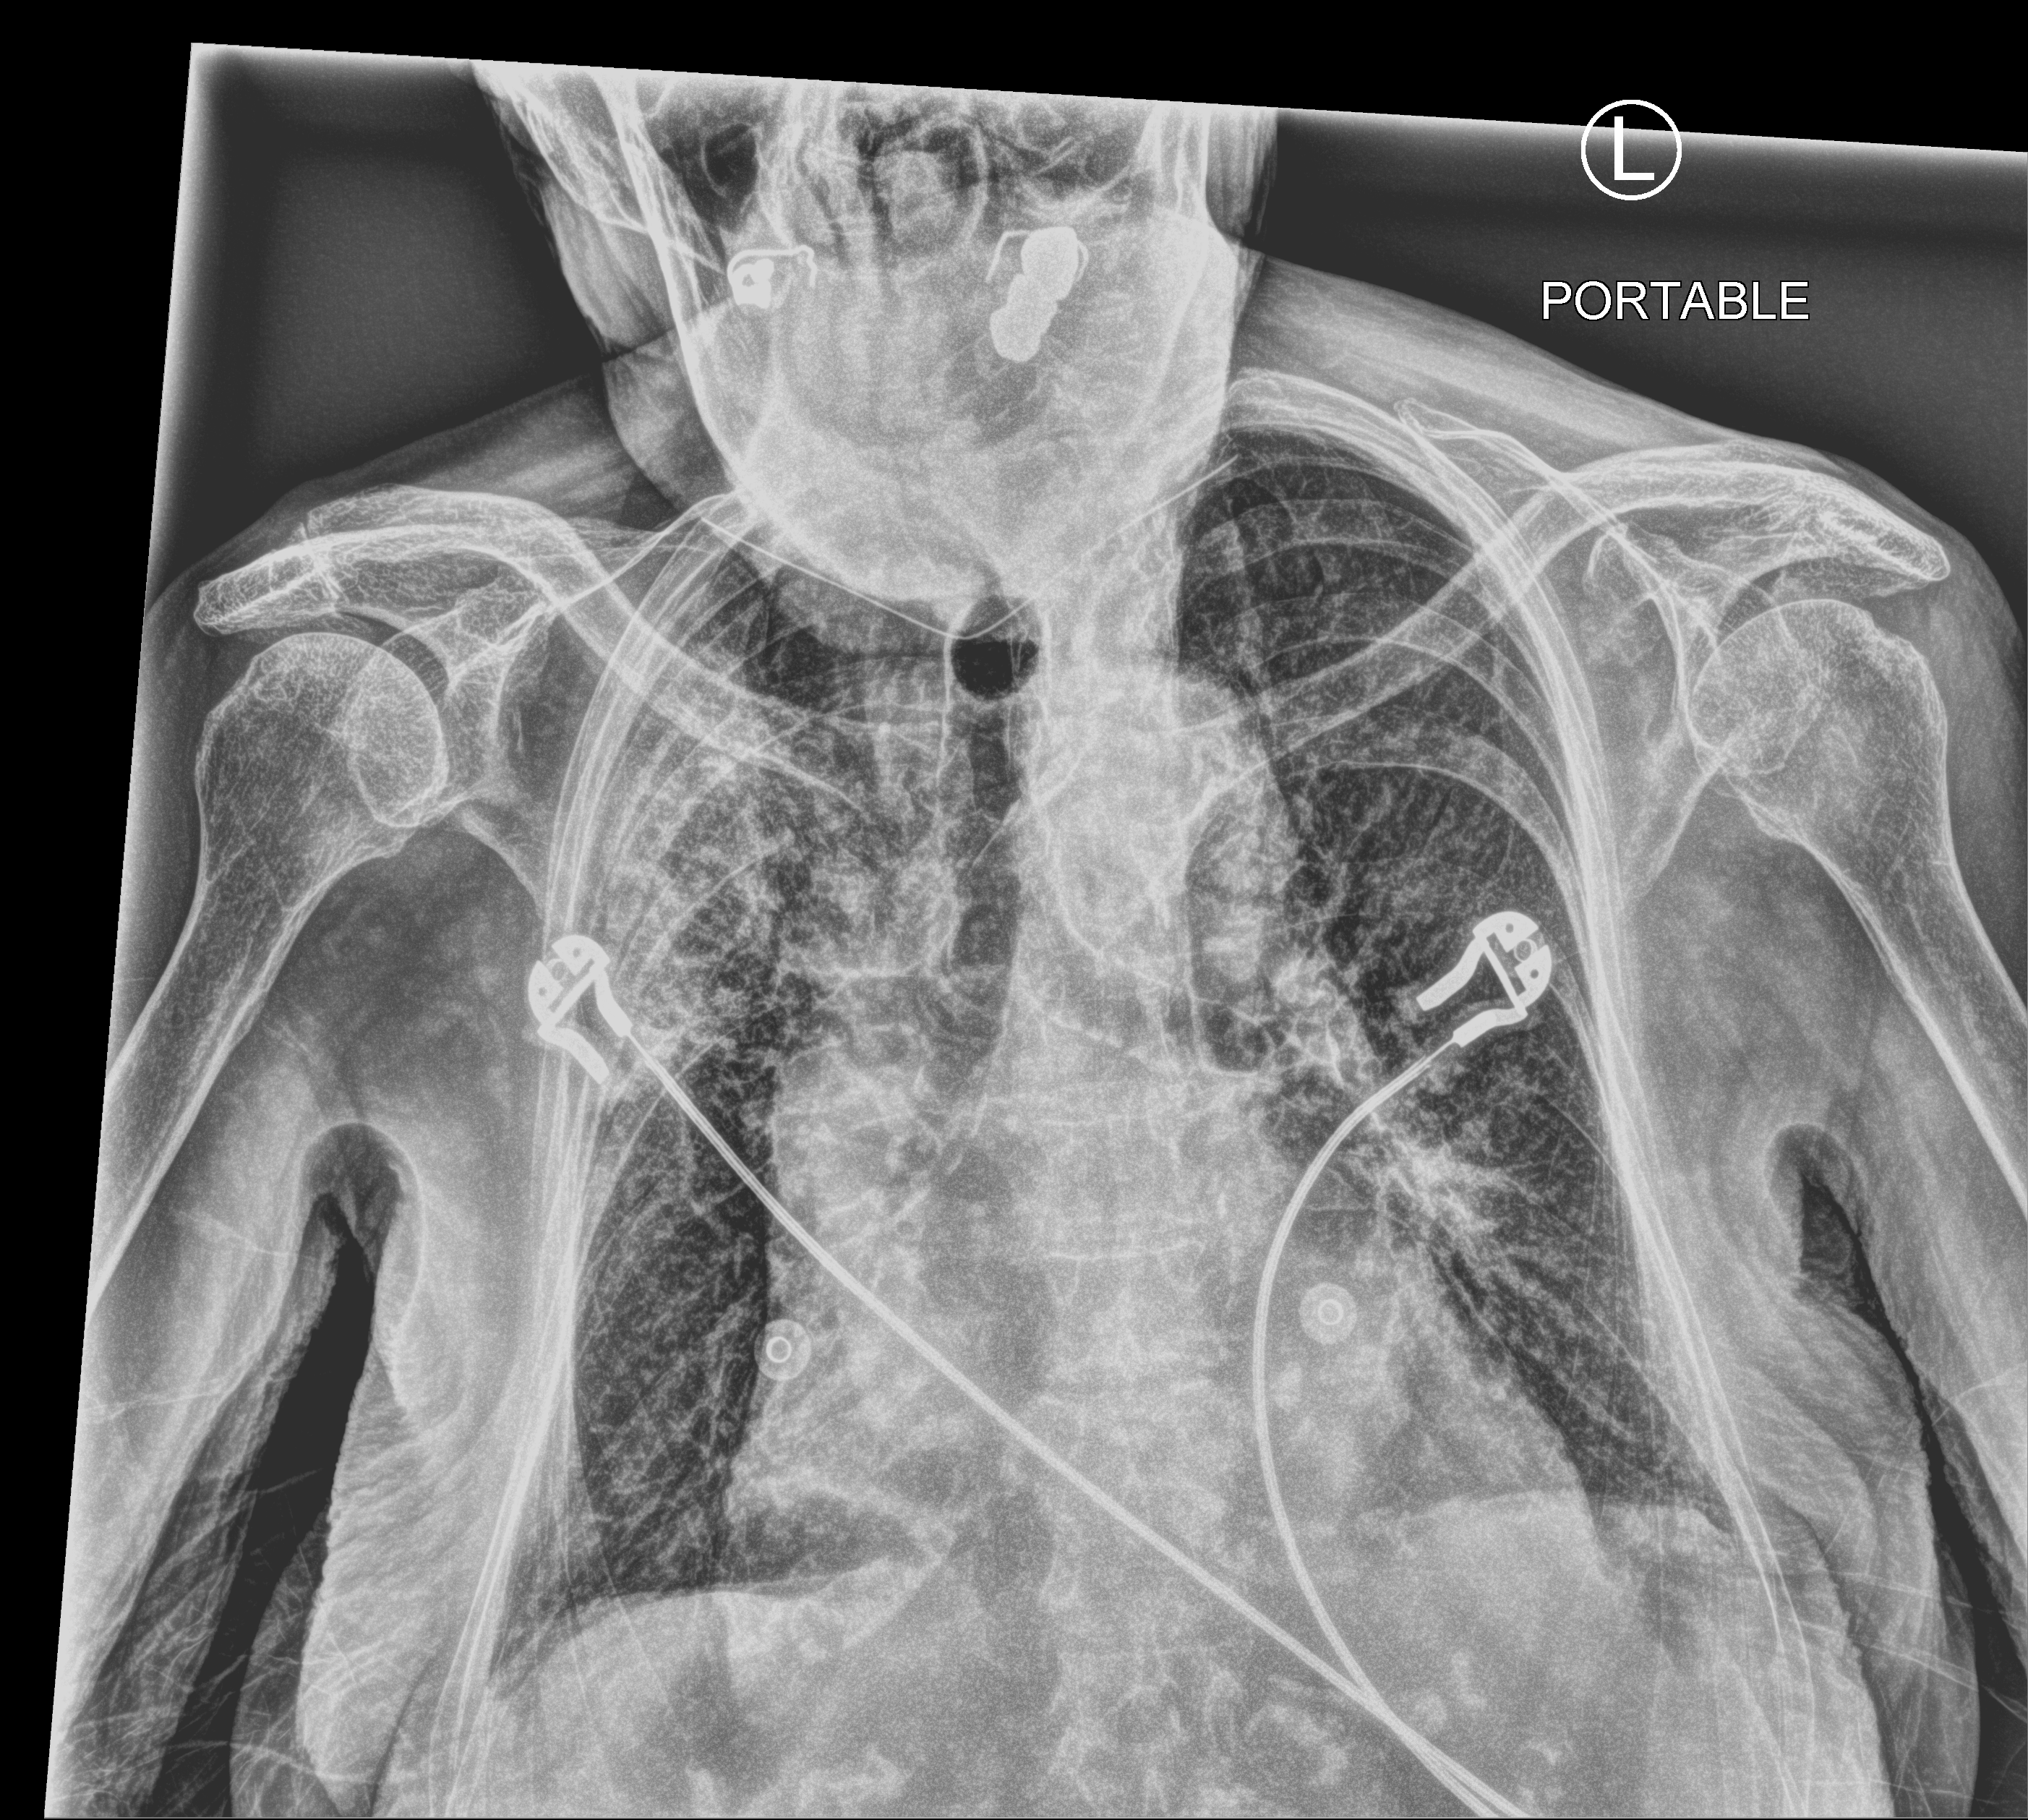
Bedside chest radiograph (computed radiography), anteroposterior (AP) projection. Female patient hospitalised with COVID-19, age 75–90 years.
From the hospital-stay record, not from the radiograph (when in the stay this image was taken is not recorded): admitted to intensive care during this hospital stay: no.